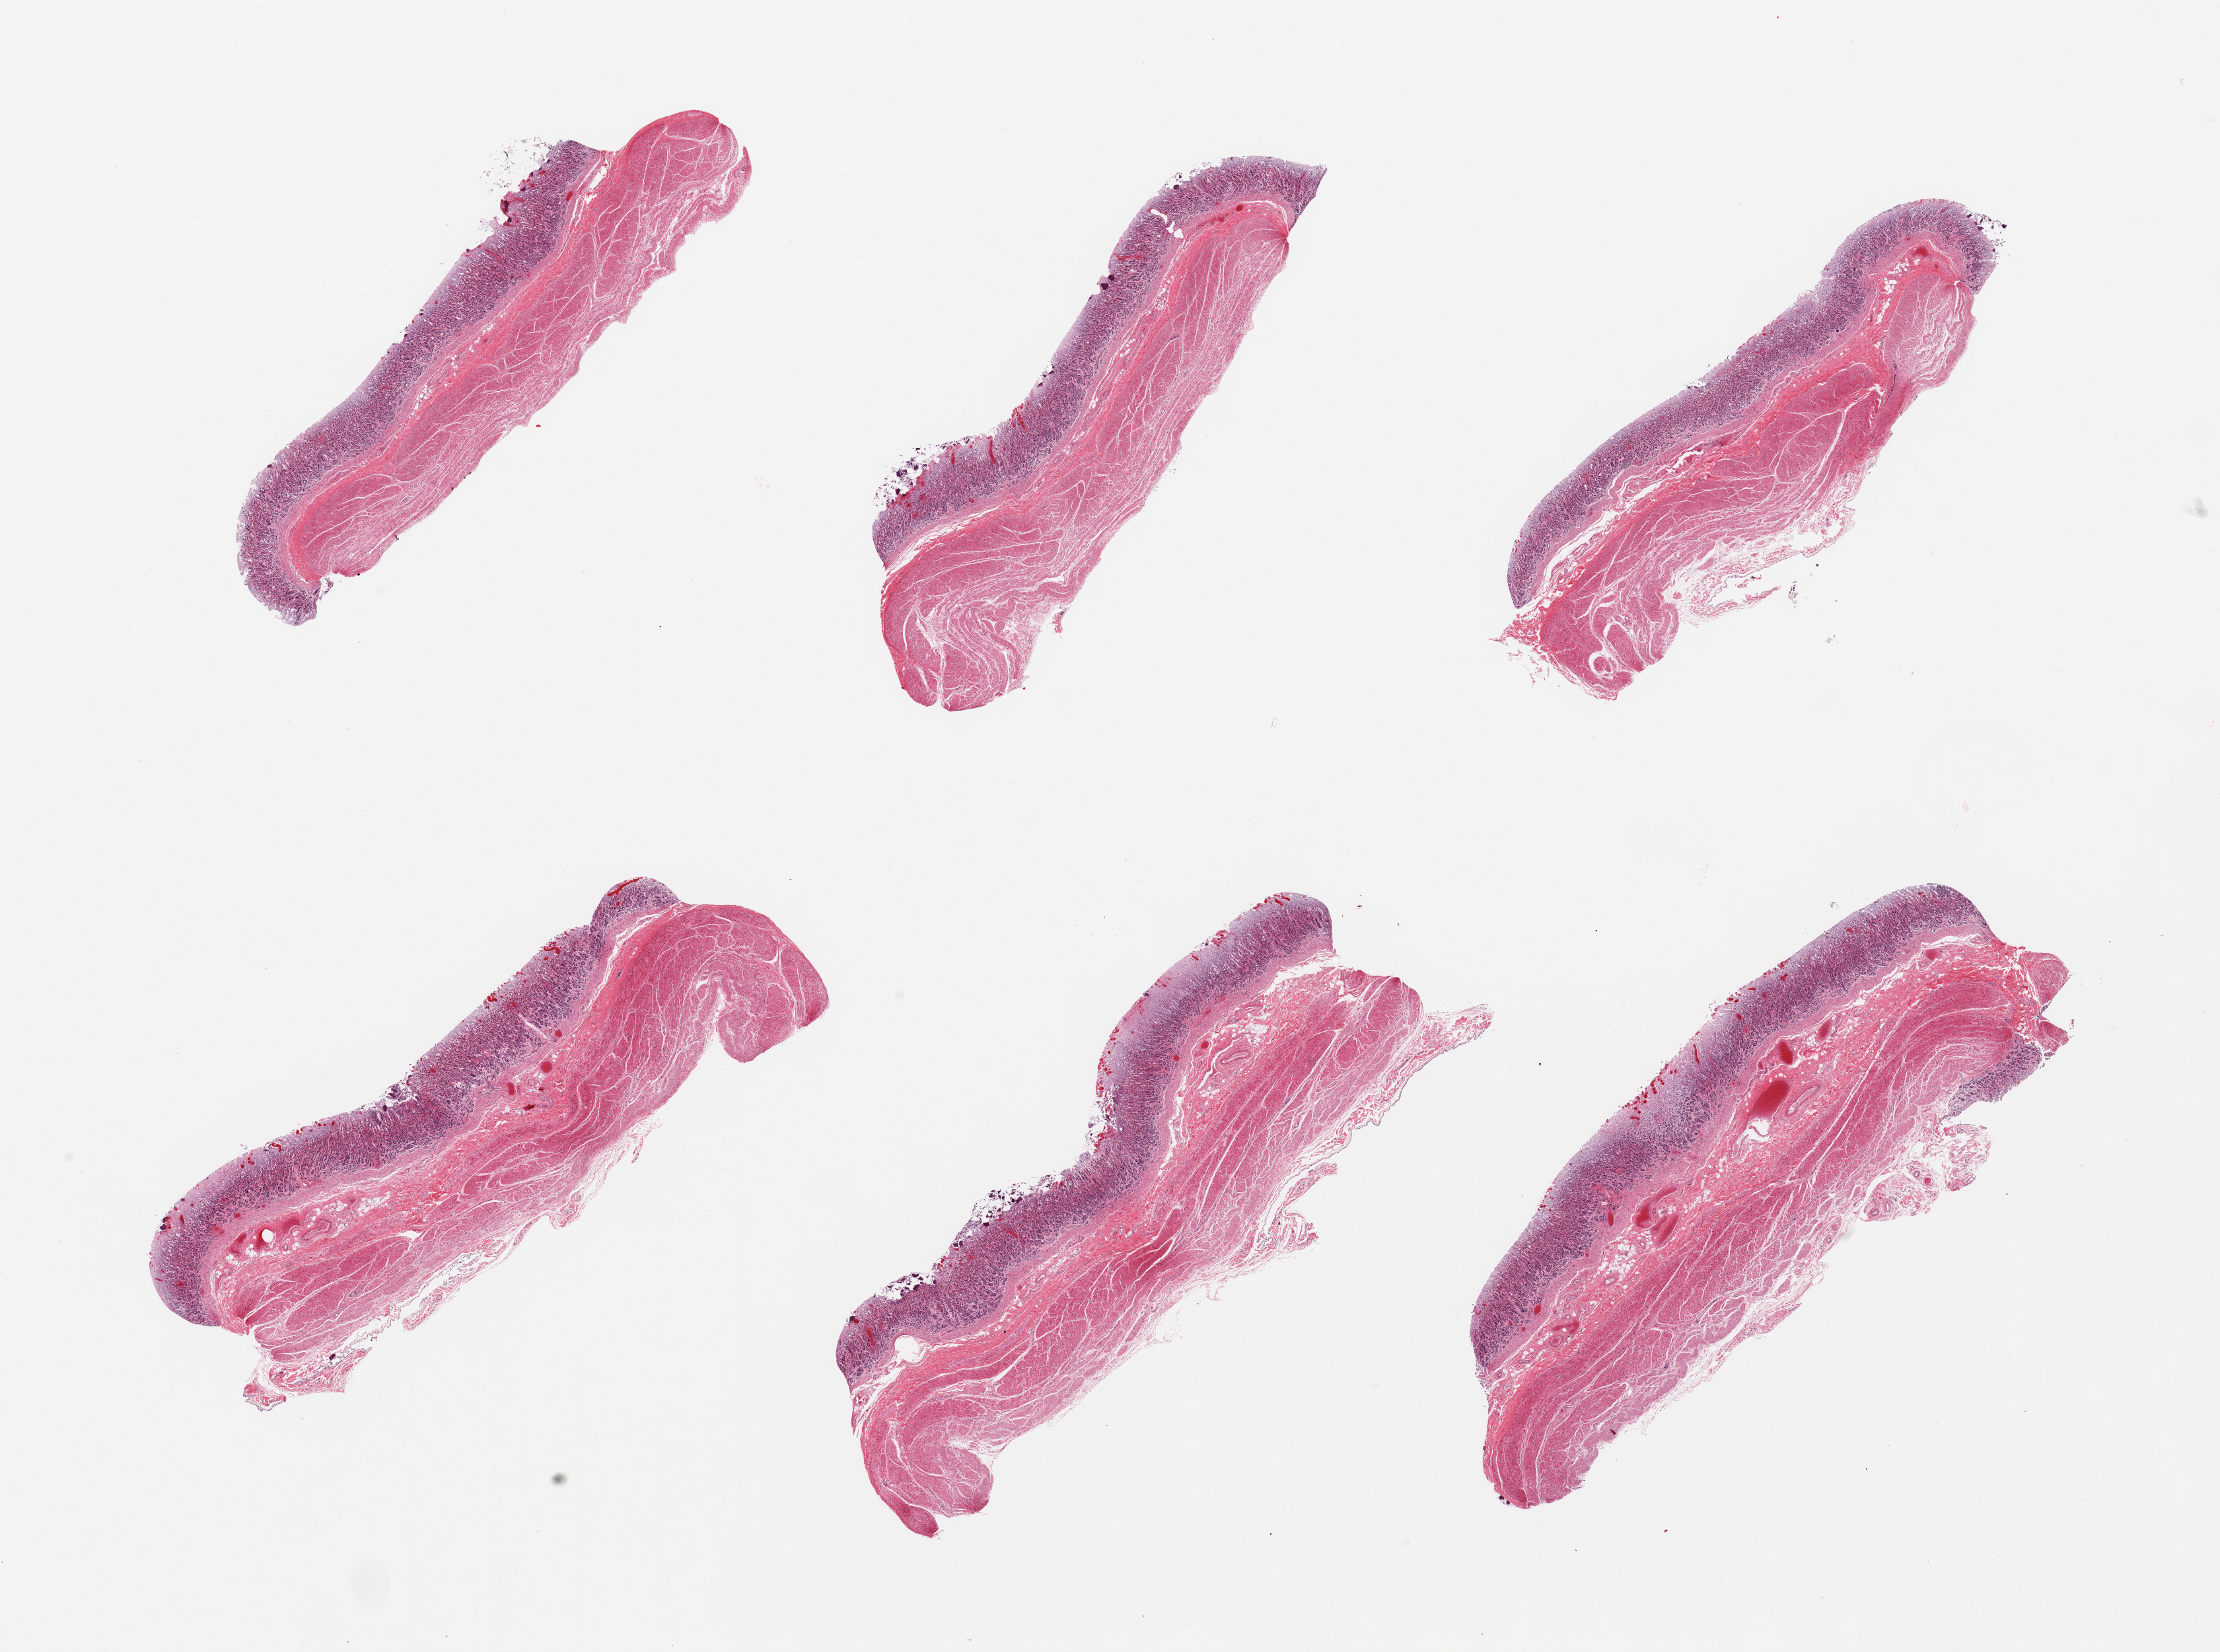
Digitized H&E-stained section, brightfield, whole scanned area (about 26.6 x 19.8 mm, acquisition: 20x scan) shown as a low-resolution overview. PAXgene-fixed, paraffin-embedded tissue. Sampled site (target tissue): stomach. Donor tissue sample. Donor sex: female.
Review note (as recorded): 6 pieces; mucosa moderately to severely autolyzed; well dissected.